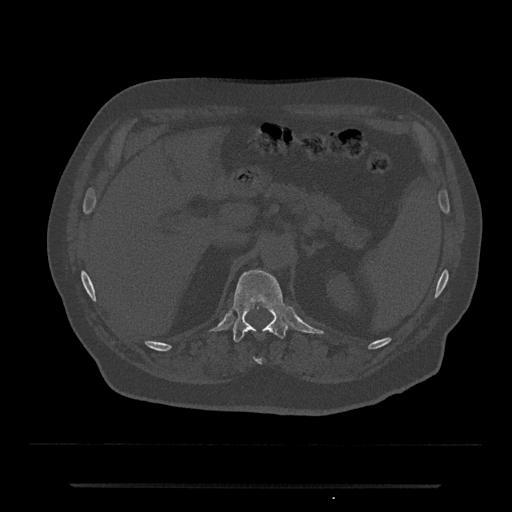
CT including the spine, one axial slice. Reconstruction kernel Br40s/3. 120 kVp. Bone window (W 1800 / L 400 HU). 512 × 512 image matrix. Male patient, age 80 years. Case-level facts recorded for this patient, not image findings: primary cancer: prostate.
Outlined on this slice (semi-automatically segmented with operator editing):
- T11 vertebra: bounding box <254,359,262,364> (left, top, right, bottom; pixels)
- T12 vertebra: <232,270,289,342>